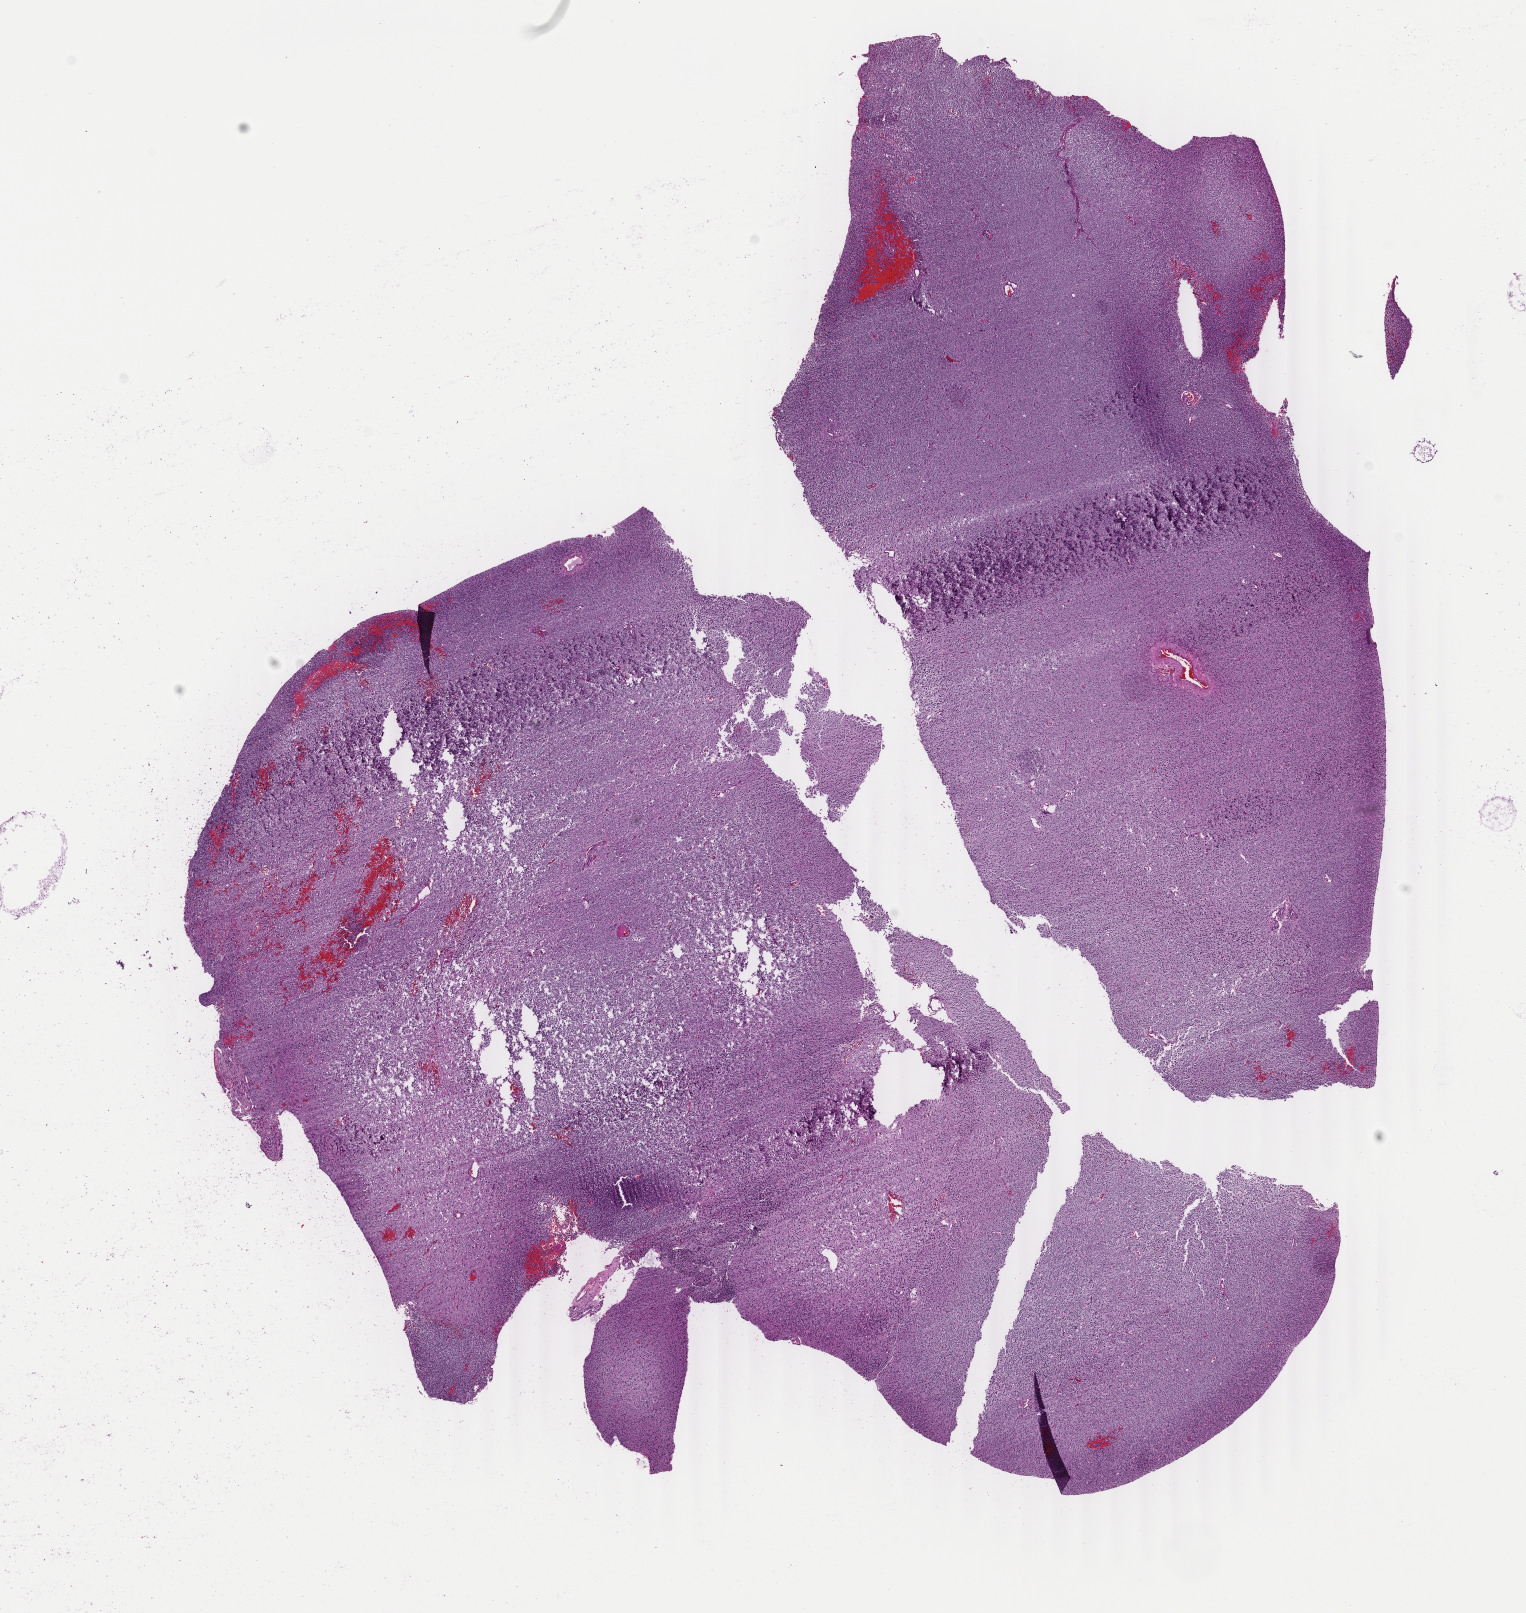
Digitized Hematoxylin and eosin (H&E) stained tissue section (whole slide), a low-resolution overview of the entire scanned area, about 12.1 x 12.8 mm (from a 40x scan), FFPE section, sample: primary tumour, brain. Patient: male, age at initial diagnosis 60 years. Histologic grade: G2 (moderately differentiated).
- histologic diagnosis: Oligodendroglioma, NOS (cerebrum)